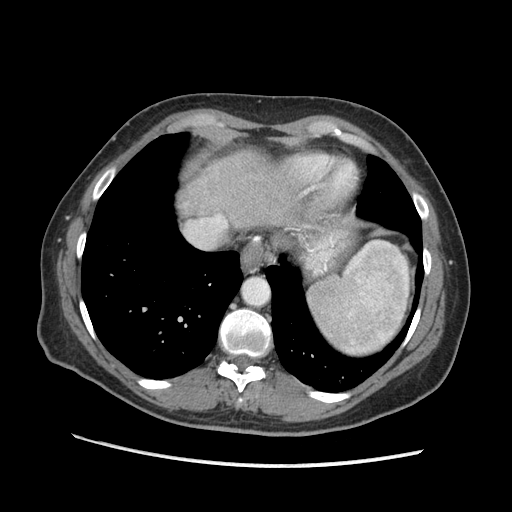
Contrast-enhanced abdominal CT (liver protocol), one axial slice. Slice 155 of 170 in the series (ordered by position). Soft-tissue window (W 400 / L 40 HU). 2.5 mm slice thickness. 512 × 512 image matrix. From the clinical record (not read from this slice): diagnosis: hepatocellular carcinoma (patient treated with transarterial chemoembolisation; whether this scan precedes or follows treatment is not stated here); TNM stage (as recorded): Stage-II; Child-Pugh class: A.
Structures marked on this image (semi-automatic segmentation, software-assisted and operator-edited):
- abdominal aorta: bounding box (x1, y1, x2, y2) in pixels: (243, 279, 269, 305)
- liver parenchyma outside the tumour (the mass and vessels are separate outlines, so this box may not span the whole liver): (178, 150, 266, 216)